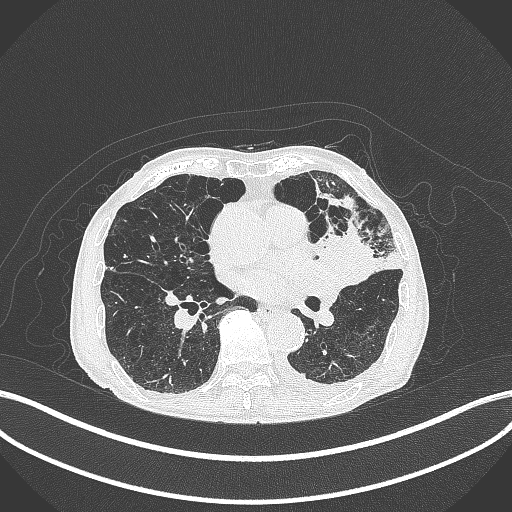
Chest CT, one axial slice; position 180 of 385 along the scan axis; 120 kVp; lung window (W 1500 / L -600 HU); 1 mm slice thickness; 512 × 512 image matrix, field of view 400 × 400 mm. Male patient, age 90 years or older. Case-level facts recorded for this patient, not image findings: clinical TNM (as recorded): T2b N1 M0.
Annotated regions visible in this slice (rectangle marked by the reading radiologist):
- lung tumour (recorded histology: squamous cell carcinoma): bounding box [x1, y1, x2, y2] px = [315, 230, 381, 289]